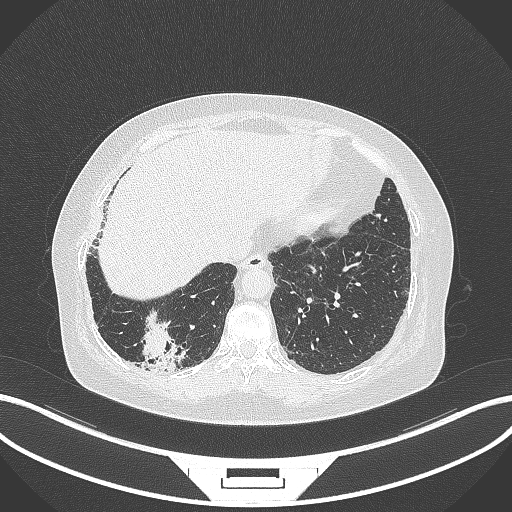
Chest CT, one axial slice; slice 35 of 296 in the series (ordered by position); lung window (W 1500 / L -600 HU); 512 × 512 image matrix, field of view 400 × 400 mm. Patient: female, 65 years. From the clinical record (not read from this slice): clinical TNM (as recorded): T2b N1 M0; histopathological grade: G1.
Outlined on this slice (bounding box drawn by a radiologist):
- lung tumour (recorded histology: adenocarcinoma): box from (x=137, y=309) to (x=190, y=372) px